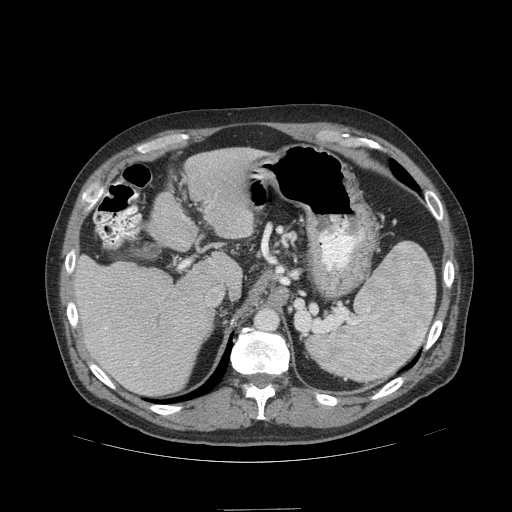
Contrast-enhanced abdominal CT (liver protocol), one axial slice; slice 71 of 99 in the series (ordered by position); 140 kVp; soft-tissue window (W 400 / L 40 HU); 2.5 mm slice thickness; 512 × 512 image matrix, field of view 440 × 440 mm. Case-level facts recorded for this patient, not image findings: diagnosis: hepatocellular carcinoma (patient treated with transarterial chemoembolisation; whether this scan precedes or follows treatment is not stated here); TNM stage (as recorded): Stage-I; Child-Pugh class: A; tumour differentiation: no biopsy.
Annotated regions visible in this slice (semi-automatic segmentation, software-assisted and operator-edited):
- liver parenchyma outside the tumour (the mass and vessels are separate outlines, so this box may not span the whole liver): bounding box (x1, y1, x2, y2) in pixels: (74, 148, 268, 396)
- liver vessels: (98, 285, 216, 390)